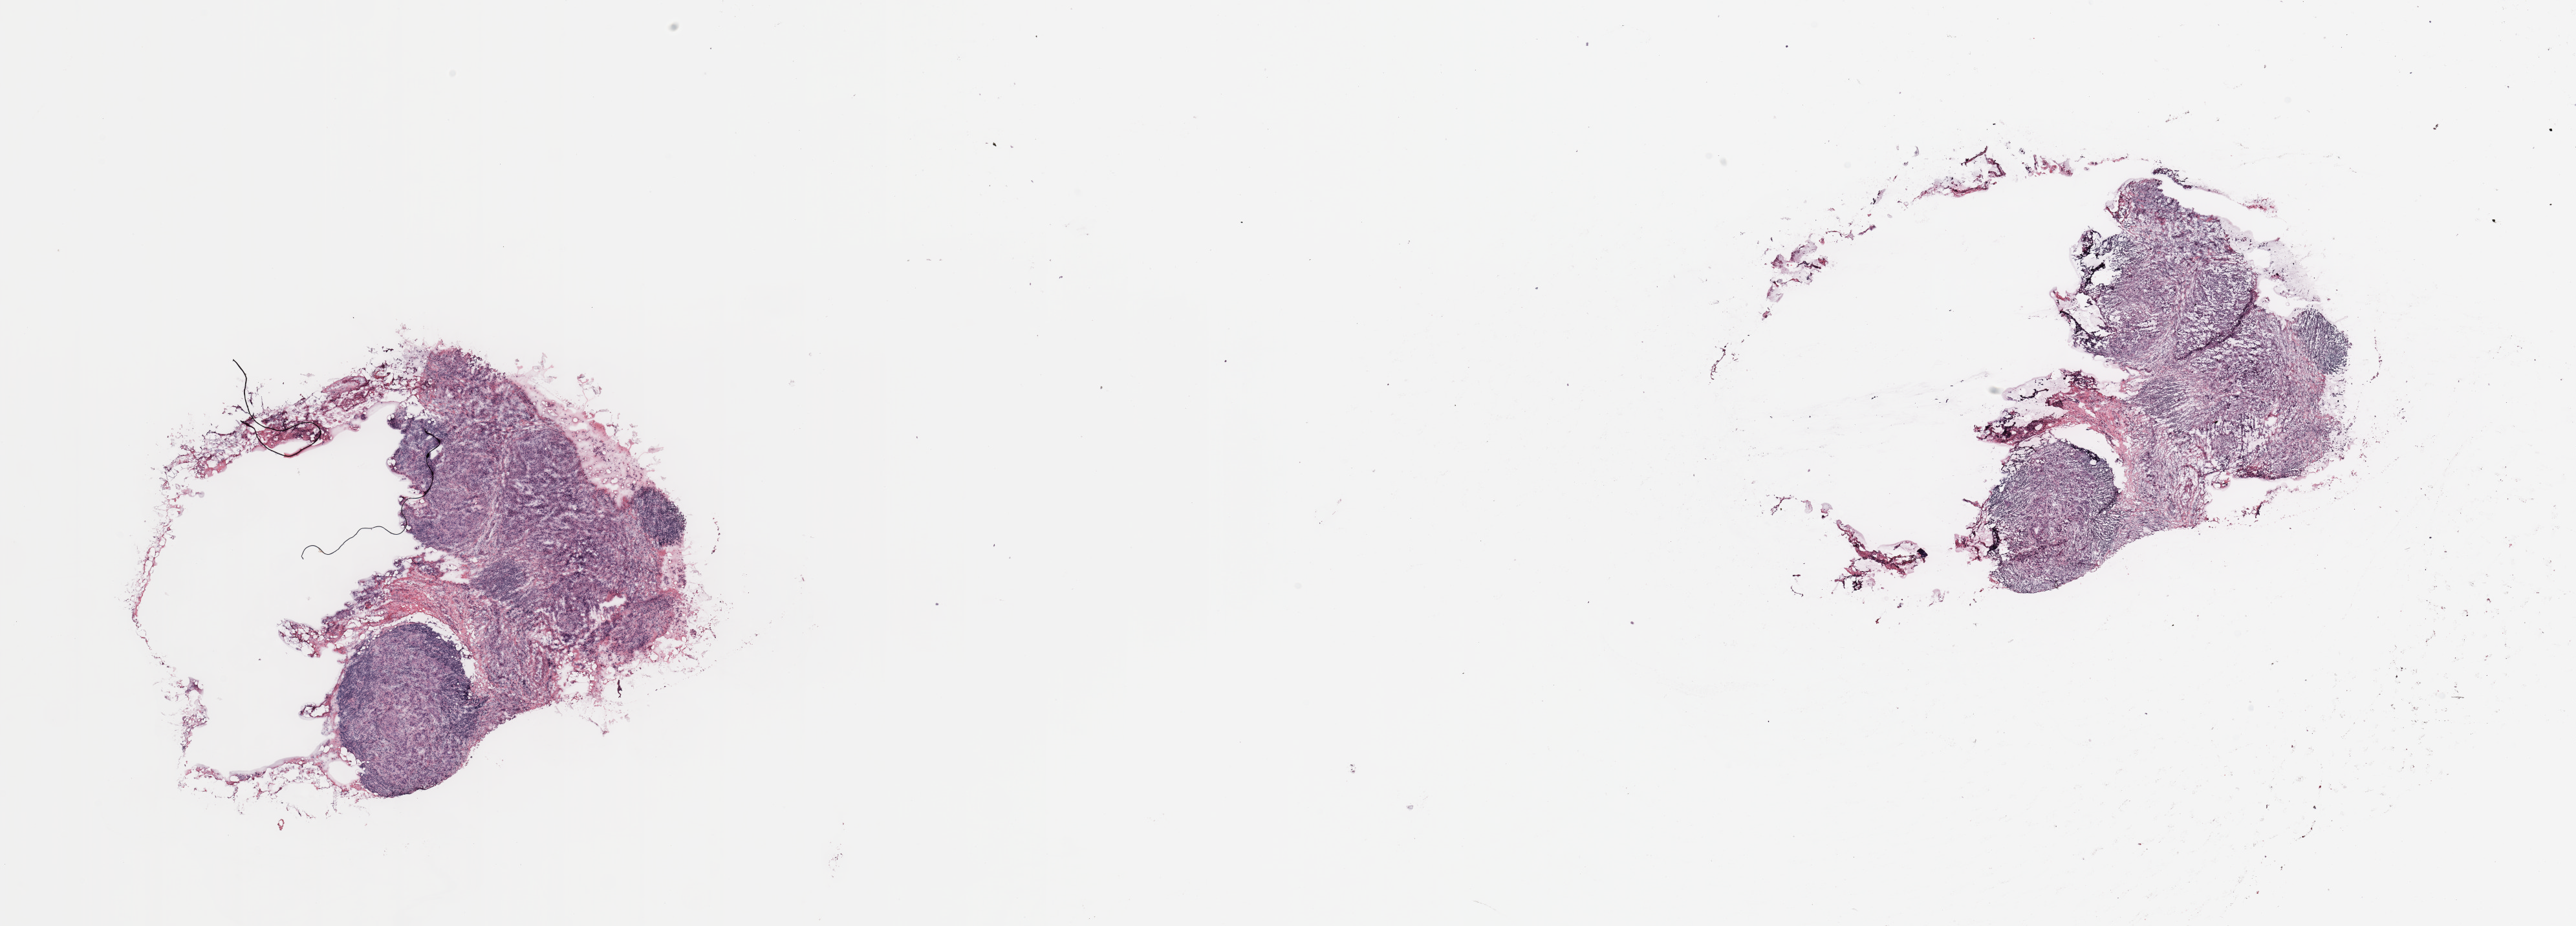
Whole-slide histology image, H&E-stained, a low-resolution overview of the entire scanned area, about 31.5 x 11.3 mm (slide scanned at 20x). Breast, tissue type not recorded.
Patient diagnosis (cohort enrolment): breast cancer (breast).